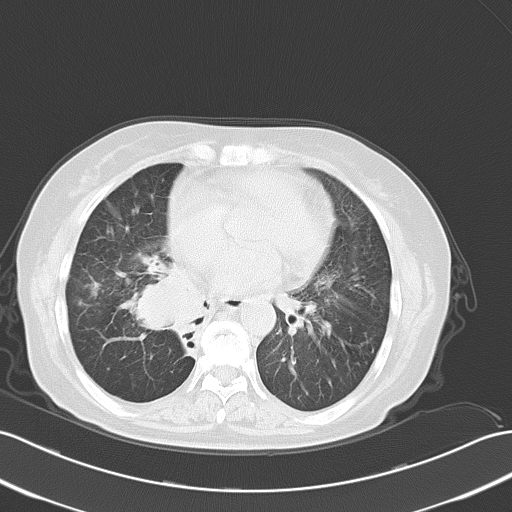
Chest CT, one axial slice; 120 kVp; lung window (W 1500 / L -600 HU); 5 mm slice thickness; 512 × 512 image matrix, field of view 353 × 353 mm. Patient: female, 65 years. Case-level facts recorded for this patient, not image findings: clinical TNM (as recorded): T1c N3 M0.
Outlined on this slice (bounding box drawn by a radiologist):
- lung tumour (recorded histology: small cell carcinoma): bounding box <125,261,204,342> (left, top, right, bottom; pixels)